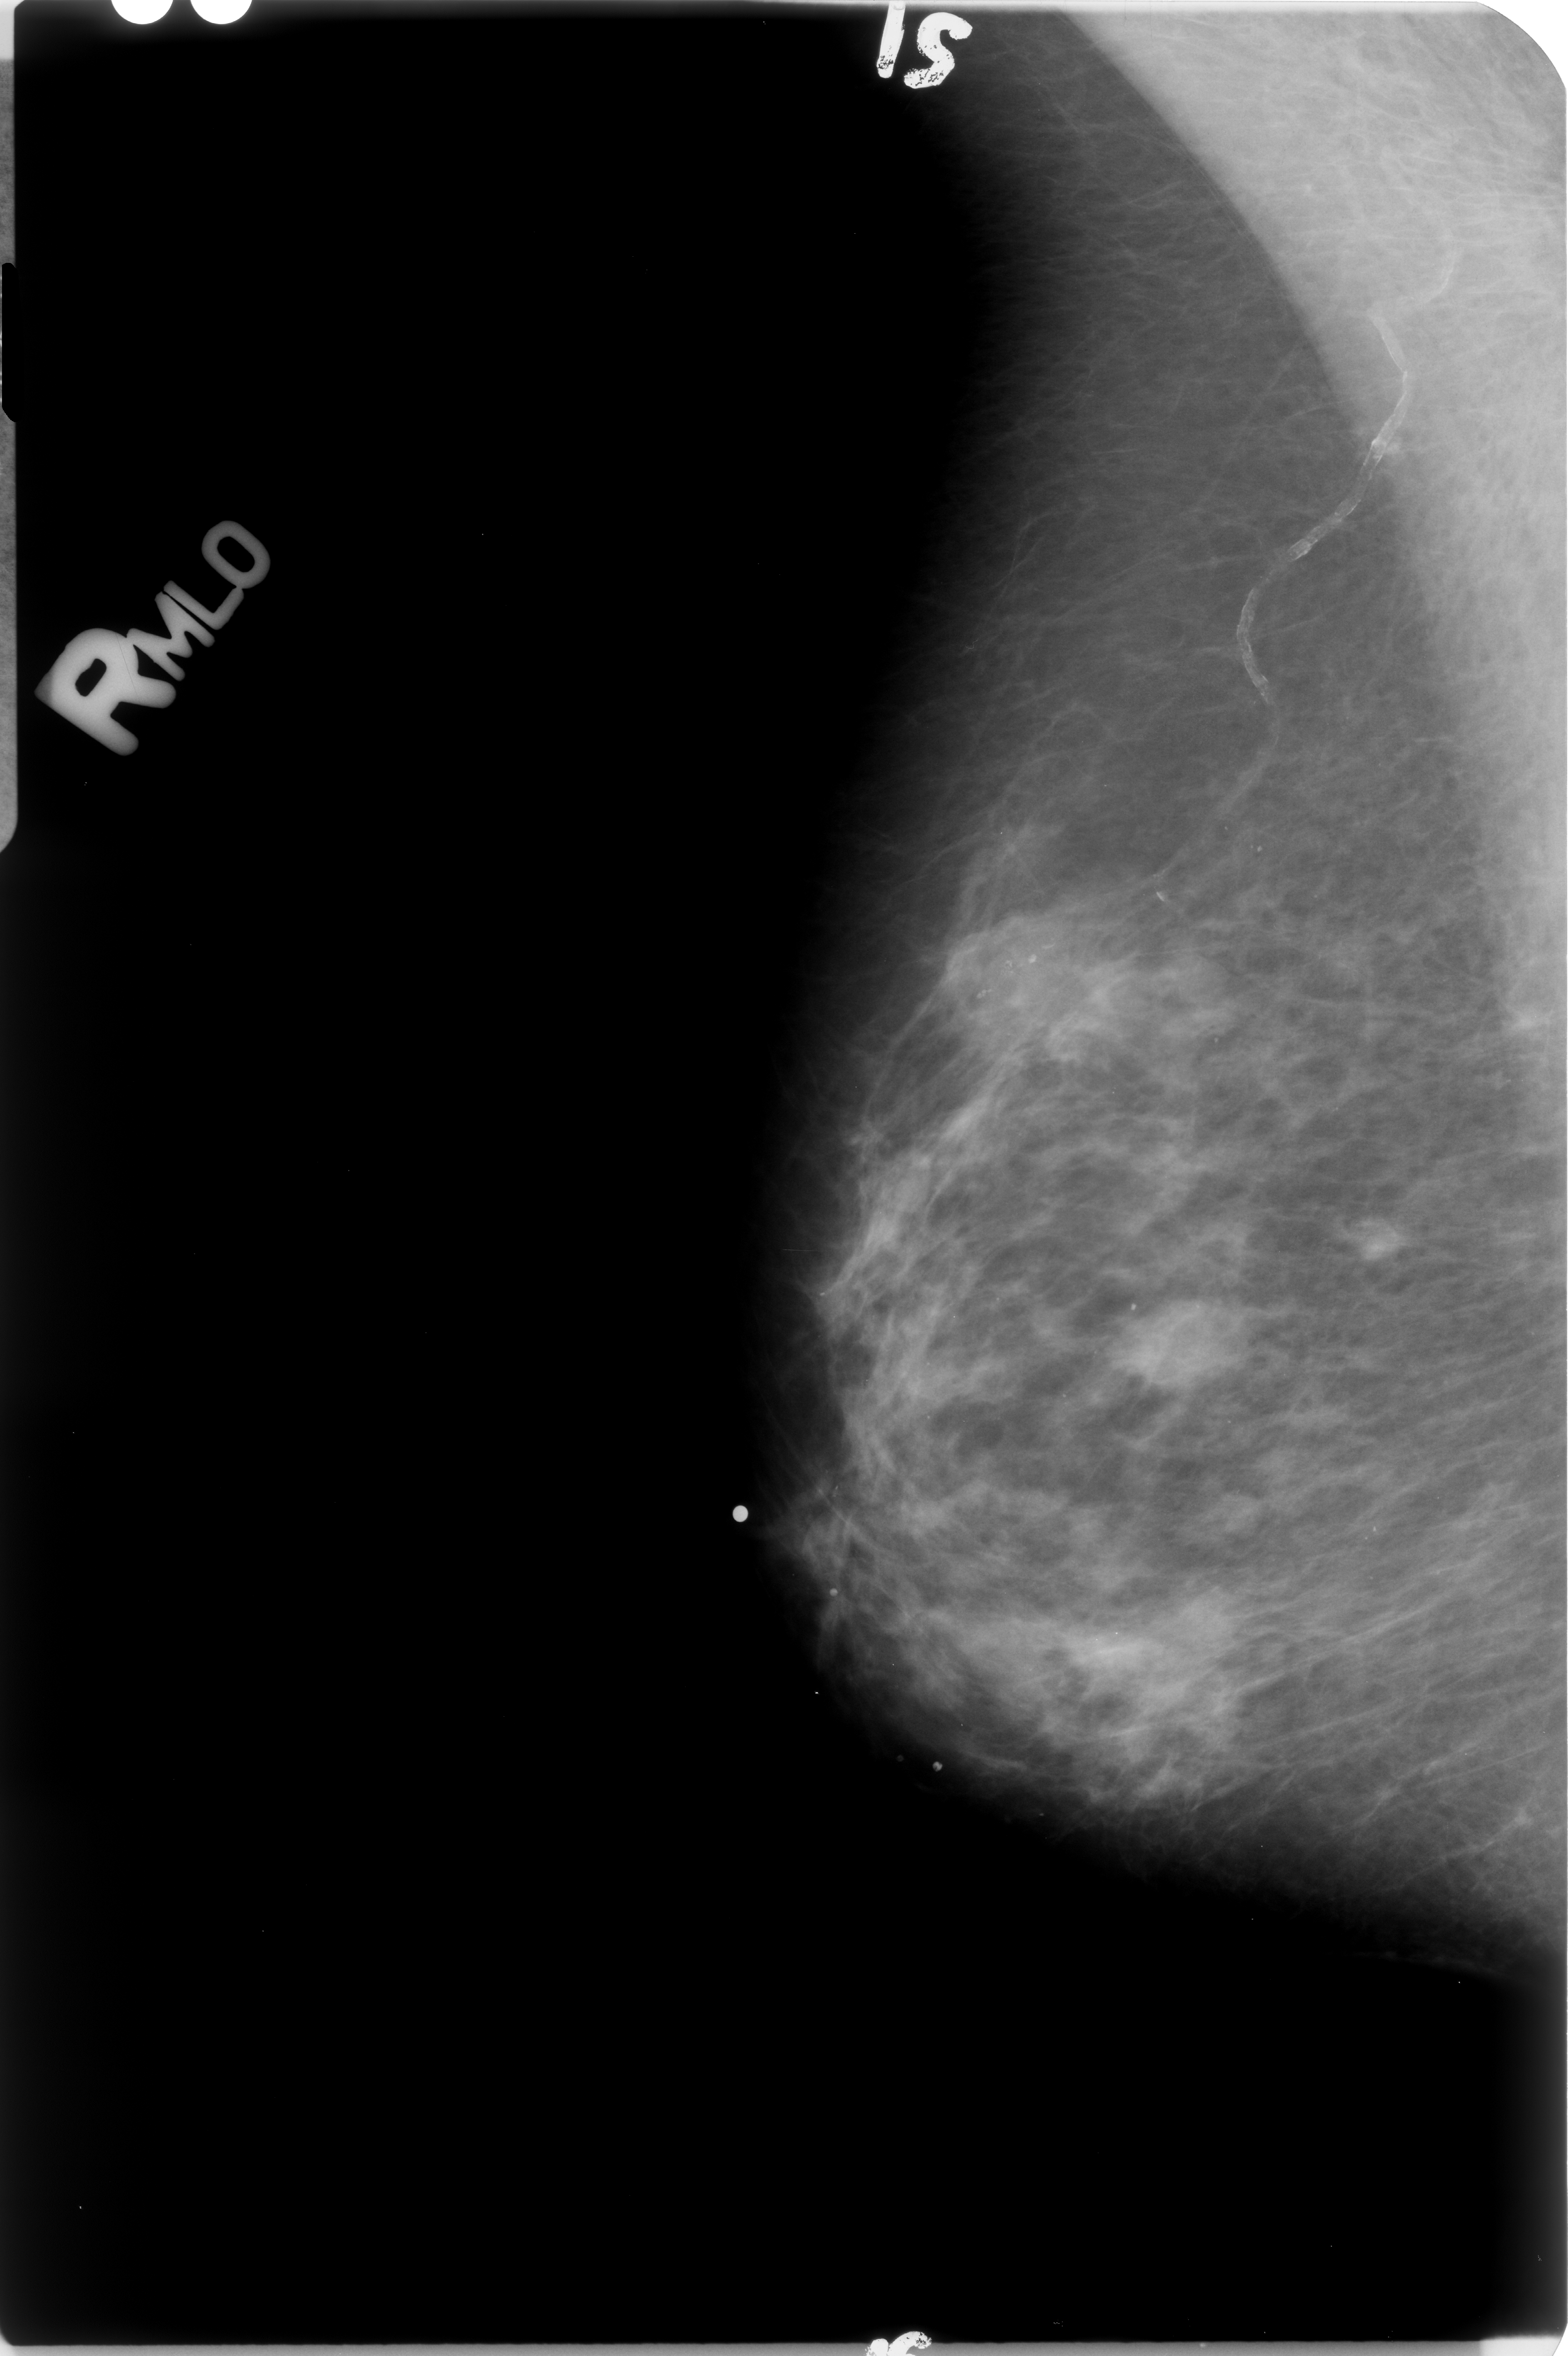
Mammogram (digitized film); right breast; MLO view; breast composition: scattered fibroglandular densities (BI-RADS density category 2 of 4).
- Finding: calcifications, morphology pleomorphic, distribution clustered; BI-RADS assessment category 4; pathology result (as recorded, not read from the image): malignant.